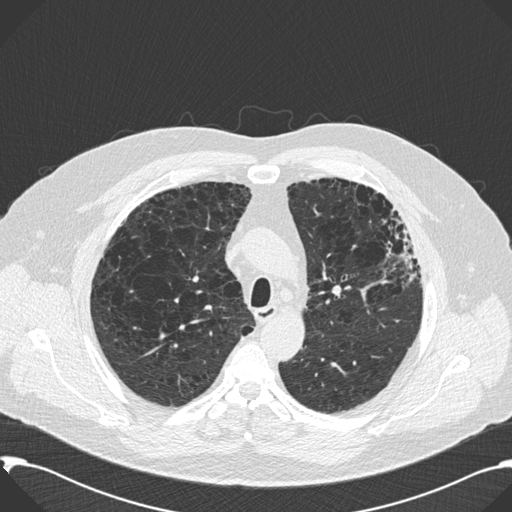
Chest CT (low-dose screening protocol), one axial image. Second annual screen. Lung window (W 1500 / L -600 HU). 2 mm slice thickness. Standard (soft-tissue) reconstruction kernel (B30f). Slice 49 of 199 in the series. 512 × 512 image matrix, field of view 380 × 380 mm. Male, age 59 years at enrolment. Current smoker at enrolment.
Lesion marked by an expert reader, bounding box [x1, y1, x2, y2] px = [362, 203, 423, 294]. Screening reader's record for this exam: no non-calcified nodule ≥4 mm recorded. Lung cancer was diagnosed 518 days after this screen: bronchiolo-alveolar carcinoma, mixed mucinous and non-mucinous, left upper lobe, stage IA (AJCC 6th edition), 20 mm at pathology.